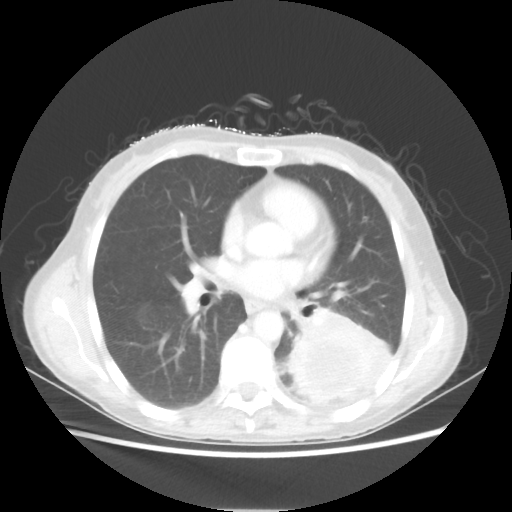
Chest CT, one axial slice. Slice 29 of 56 in the series (ordered by position). Reconstruction kernel STANDARD. 80 kVp. Lung window (W 1500 / L -600 HU). 5 mm slice thickness. 512 × 512 image matrix. Female patient, age 53 years. Case-level facts recorded for this patient, not image findings: clinical TNM (as recorded): T3 N0 M0.
Outlined on this slice (bounding box drawn by a radiologist):
- lung tumour (recorded histology: adenocarcinoma): bounding box <286,310,391,404> (left, top, right, bottom; pixels)